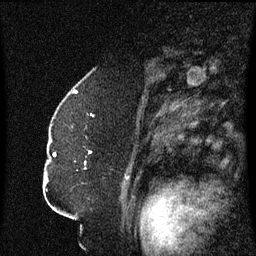
Breast MRI (dynamic contrast-enhanced), one sagittal slice. Position 44 of 60 along the scan axis. Dynamic contrast-enhanced series, image 2 of 3 at this slice position (ordered by acquisition). 1.5 T. TE 4.2 ms, TR 8.4 ms. 256 × 256 image matrix, field of view 200 × 200 mm. Patient: female, 52 years. Case-level facts recorded for this patient, not image findings: setting: breast cancer imaged before/during neoadjuvant chemotherapy; receptor status: HR-positive, HER2-negative.
Annotated regions visible in this slice (semi-automatically segmented with operator editing):
- analysis volume of interest (the breast-tissue region the enhancement analysis was run in; not a lesion): box from (x=49, y=124) to (x=125, y=187) px
- tumour enhancement mask (voxels above the 70 % enhancement threshold inside the analysis volume of interest): (x=54, y=152)–(x=92, y=165)